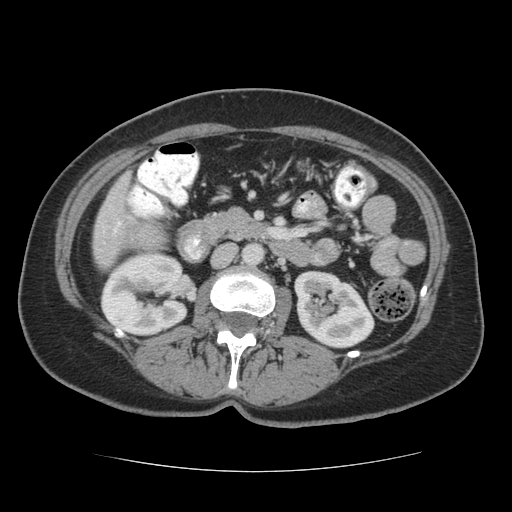
Contrast-enhanced abdominal CT (liver protocol), one axial slice; position 13 of 75 along the scan axis; reconstruction kernel STANDARD; 140 kVp; soft-tissue window (W 400 / L 40 HU); 512 × 512 image matrix. From the clinical record (not read from this slice): diagnosis: hepatocellular carcinoma (patient treated with transarterial chemoembolisation; whether this scan precedes or follows treatment is not stated here); TNM stage (as recorded): Stage-I; Child-Pugh class: A.
Structures marked on this image (semi-automatically segmented with operator editing):
- liver parenchyma outside the tumour (the mass and vessels are separate outlines, so this box may not span the whole liver): bounding box (x1, y1, x2, y2) in pixels: (94, 170, 146, 266)
- liver vessels: (104, 205, 122, 235)